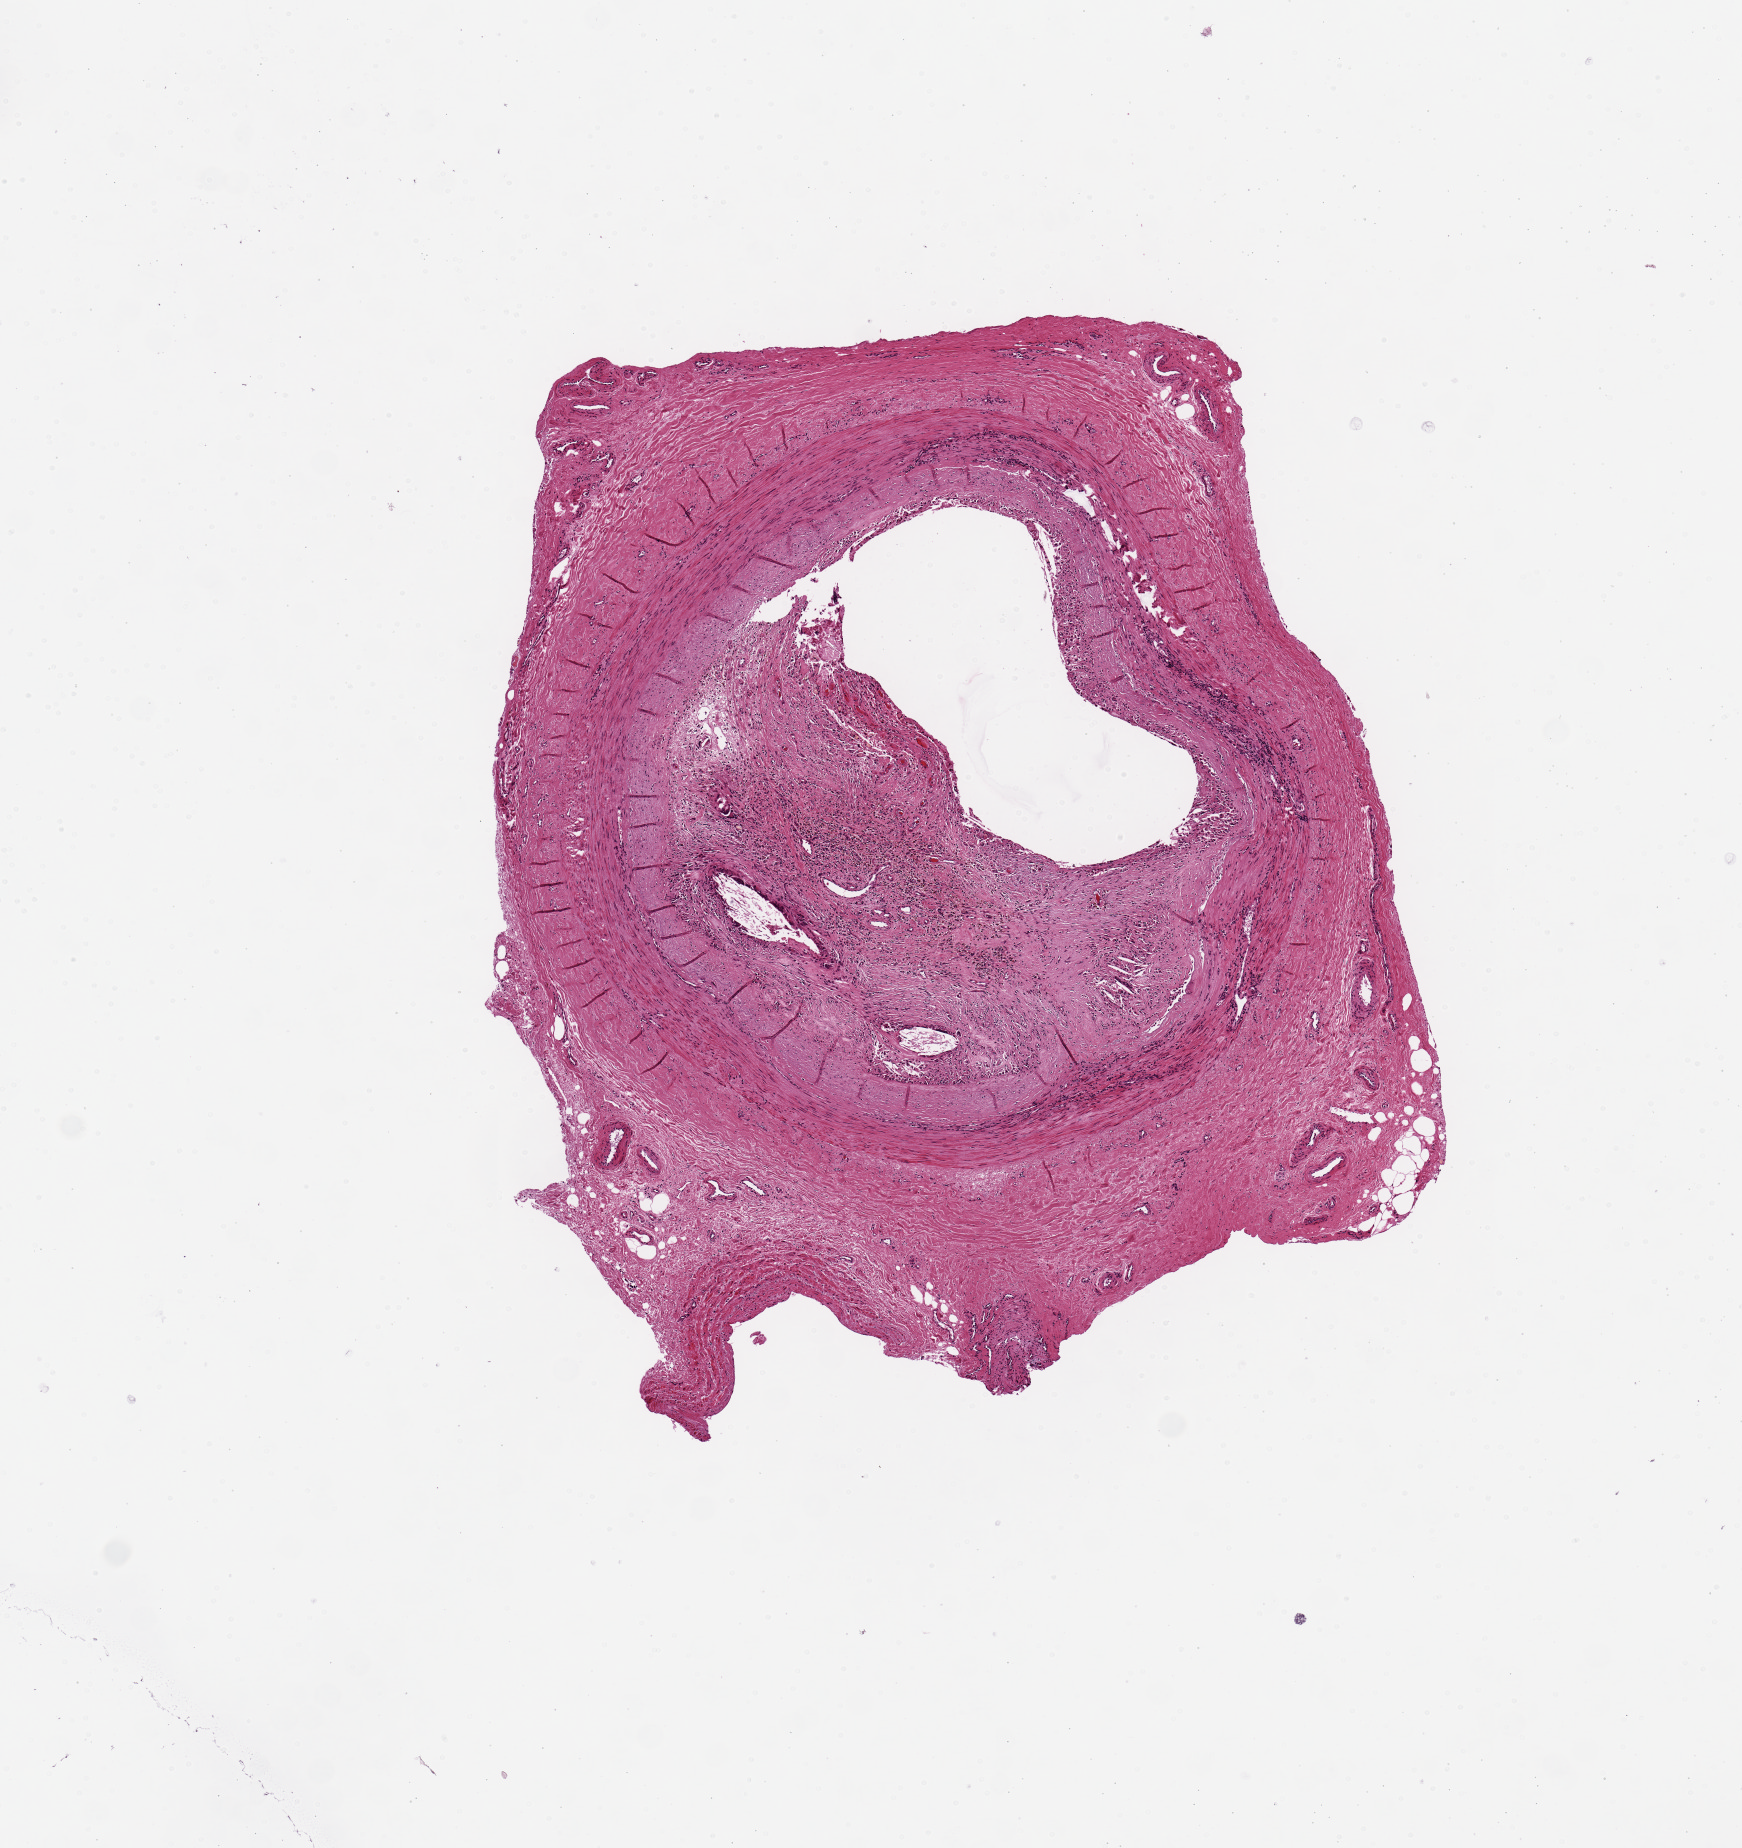
Haematoxylin and eosin whole-slide image — a low-resolution overview of the entire scanned area, about 6.9 x 7.3 mm; PAXgene-fixed paraffin-embedded (PFPE) section; sampled site (target tissue): tibial artery; tissue donor sample.
Reviewer comment on this tissue sample: Artery with 60% occlusion by atheromatous plaque.